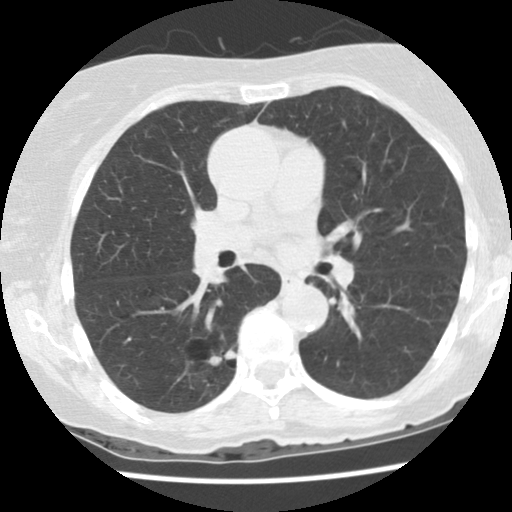
Low-dose screening chest CT, one axial slice. Position 80 of 136 along the scan axis. Reconstruction kernel STANDARD. 120 kVp. Lung window (W 1500 / L -600 HU). 2.5 mm slice thickness. 512 × 512 image matrix, field of view 300 × 300 mm.
Outlined on this slice (manually delineated by an expert):
- lesion 1 (tumor, lower lobe of right lung): bounding box [x1, y1, x2, y2] px = [210, 351, 237, 365]